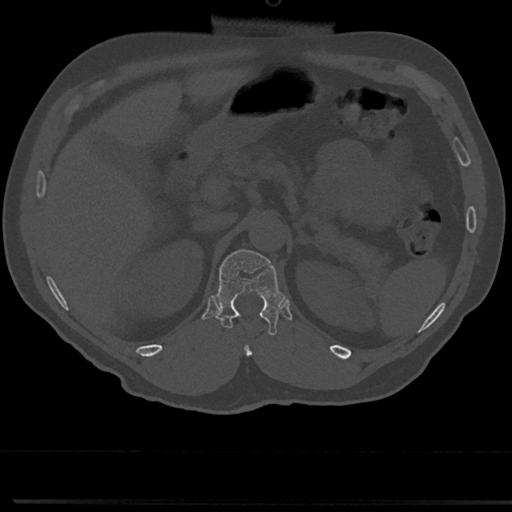
CT including the spine, one axial slice; slice 154 of 817 in the series (ordered by position); reconstruction kernel Br40s/3; bone window (W 1800 / L 400 HU); 512 × 512 image matrix. Patient: male, 61 years. Case-level facts recorded for this patient, not image findings: primary cancer: prostate.
Annotated regions visible in this slice (semi-automatic segmentation, software-assisted and operator-edited):
- T12 vertebra: box from (x=215, y=247) to (x=281, y=333) px